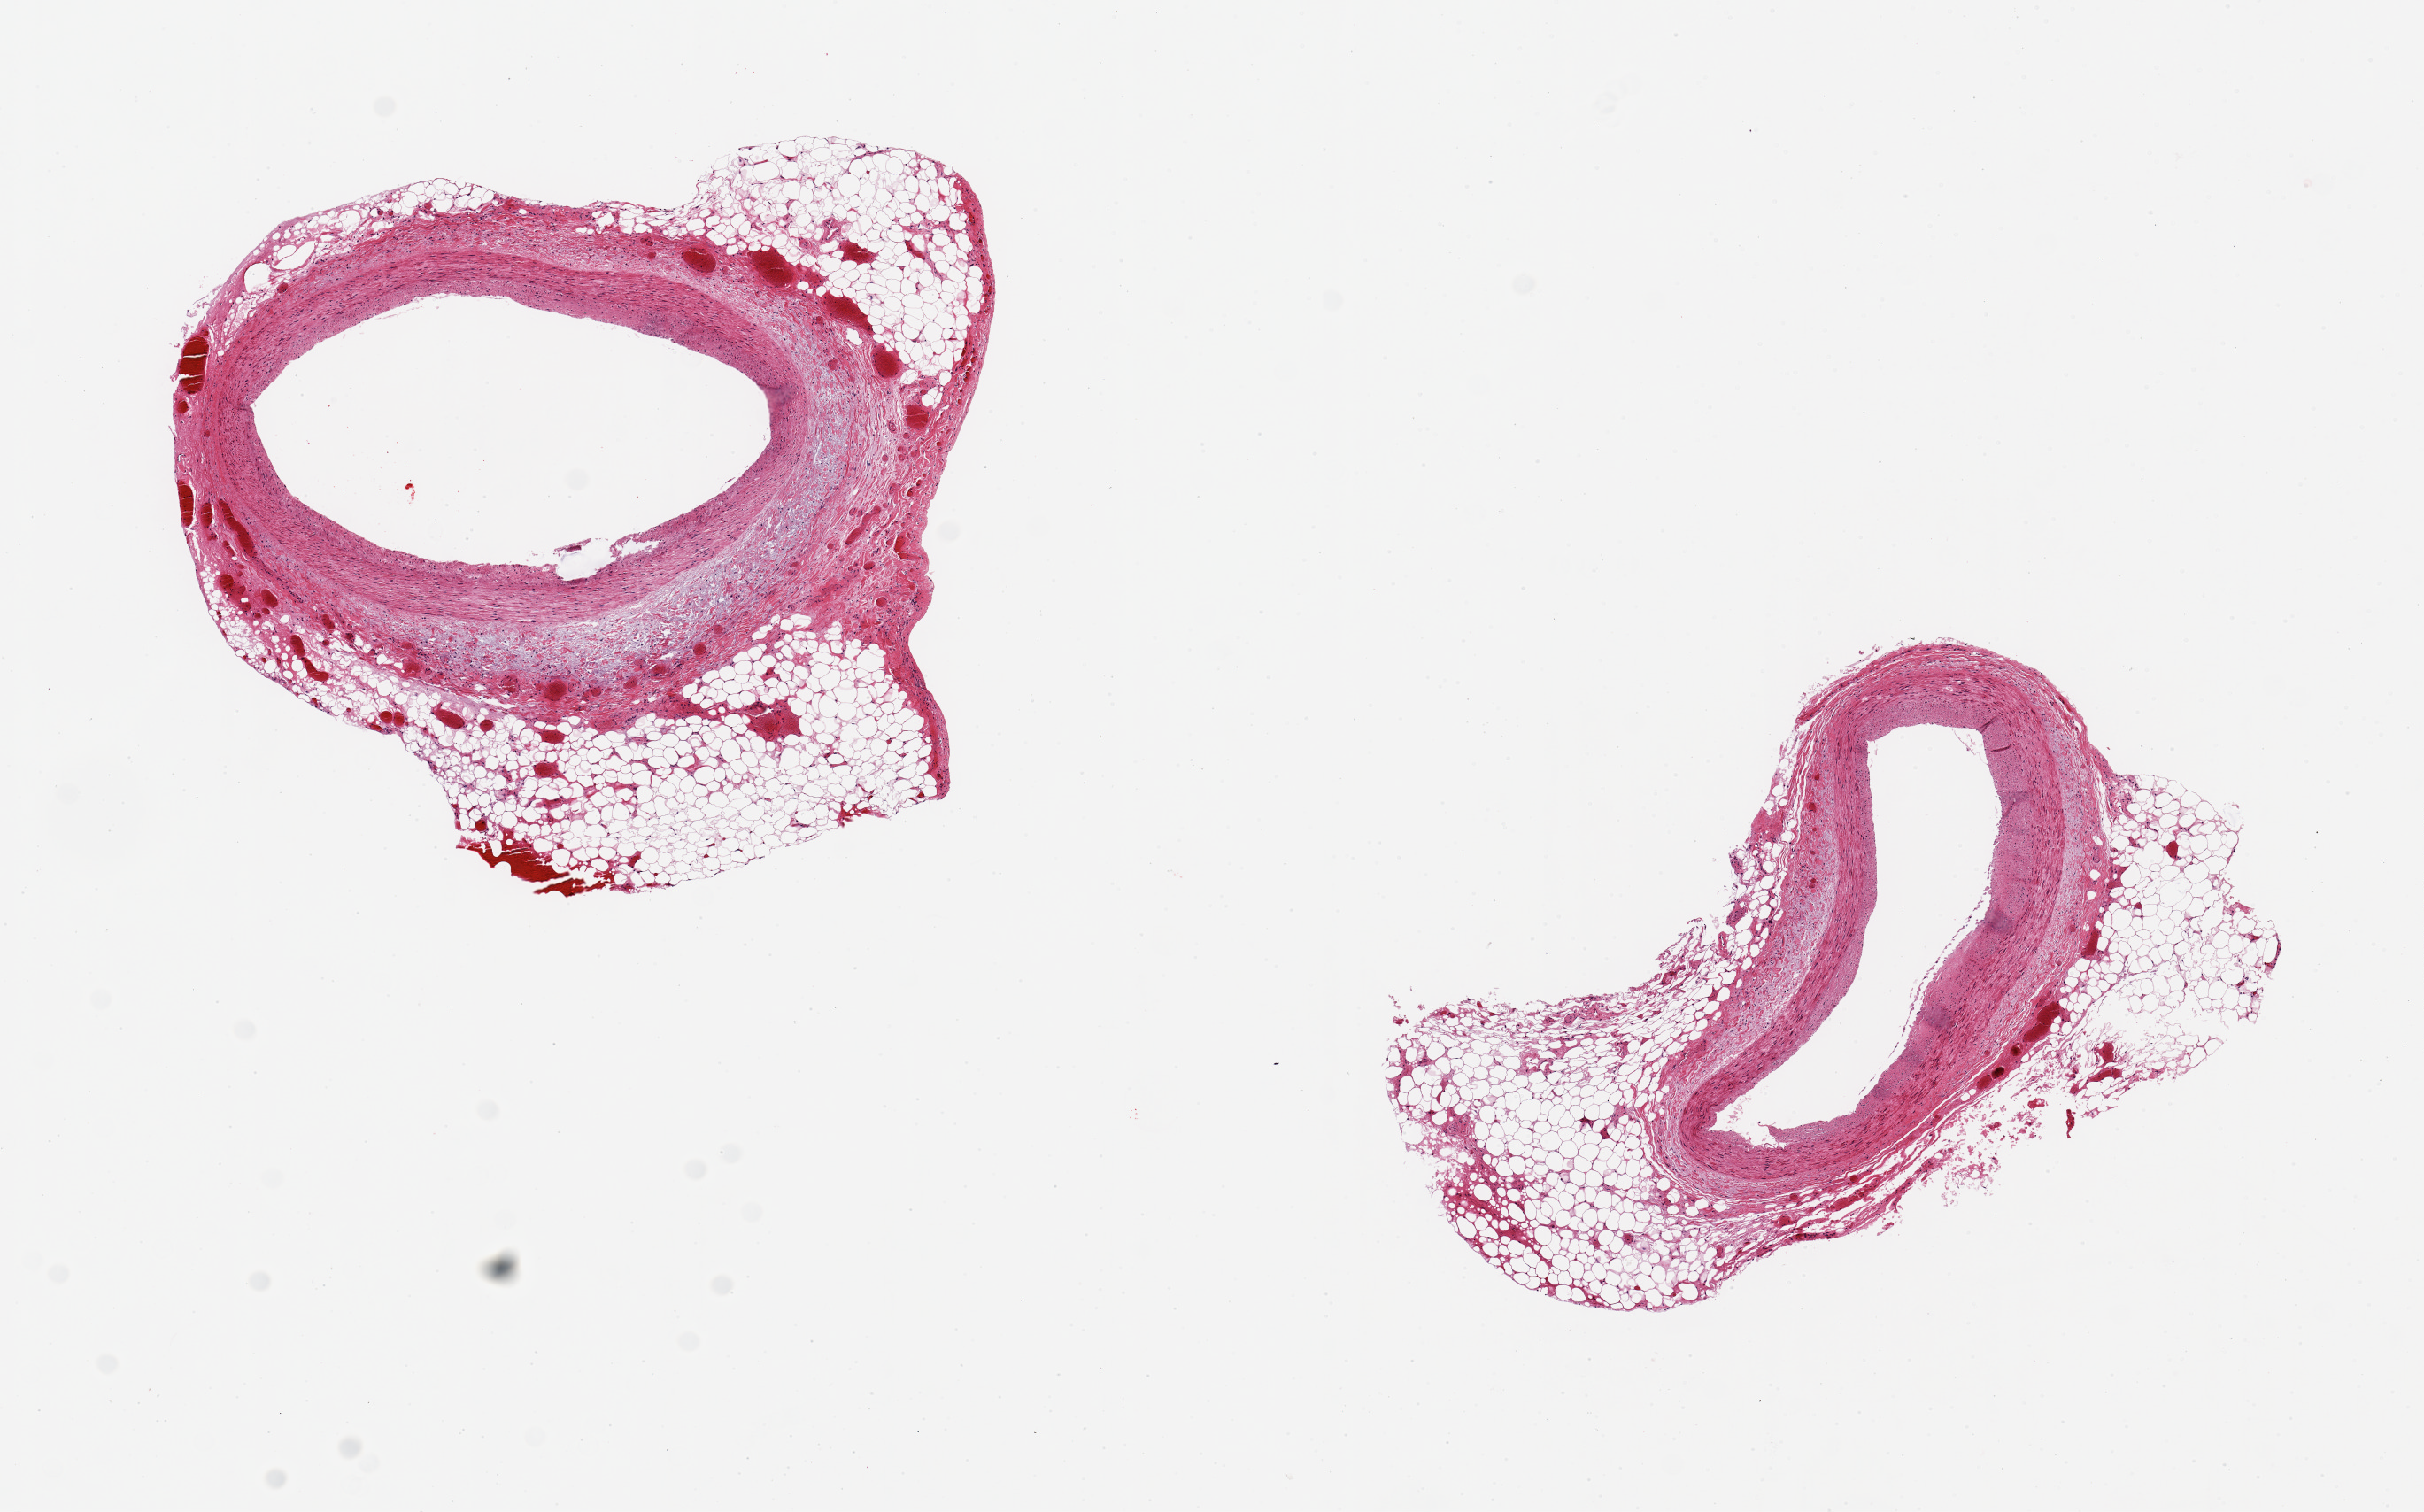
H&E whole-slide image — shown as a low-resolution overview of the whole scanned area (about 10.8 x 6.8 mm), PAXgene-fixed, paraffin-embedded tissue, sampled site (target tissue): coronary artery, donor tissue sample.
Pathologist's review note for this sample: 2 aliquots, ~2.5mm d., both with discontinuous rim of adherent fat up to 1.1mm.